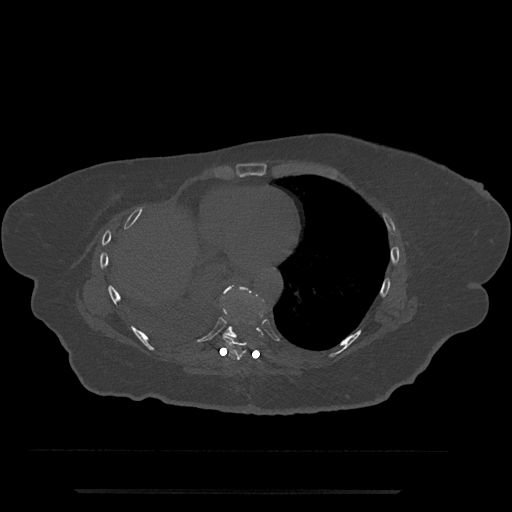
CT including the spine, one axial slice. Position 373 of 797 along the scan axis. Reconstruction kernel Br40s/3. 120 kVp. Bone window (W 1800 / L 400 HU). 0.5 mm slice thickness. 512 × 512 image matrix. Patient: female, 51 years. From the clinical record (not read from this slice): primary cancer: neuro; vertebrae with lytic lesions (as recorded): T8.
Structures marked on this image (semi-automatically segmented with operator editing):
- T8 vertebra: bounding box <222,294,263,360> (left, top, right, bottom; pixels)
- T9 vertebra: <218,285,265,339>